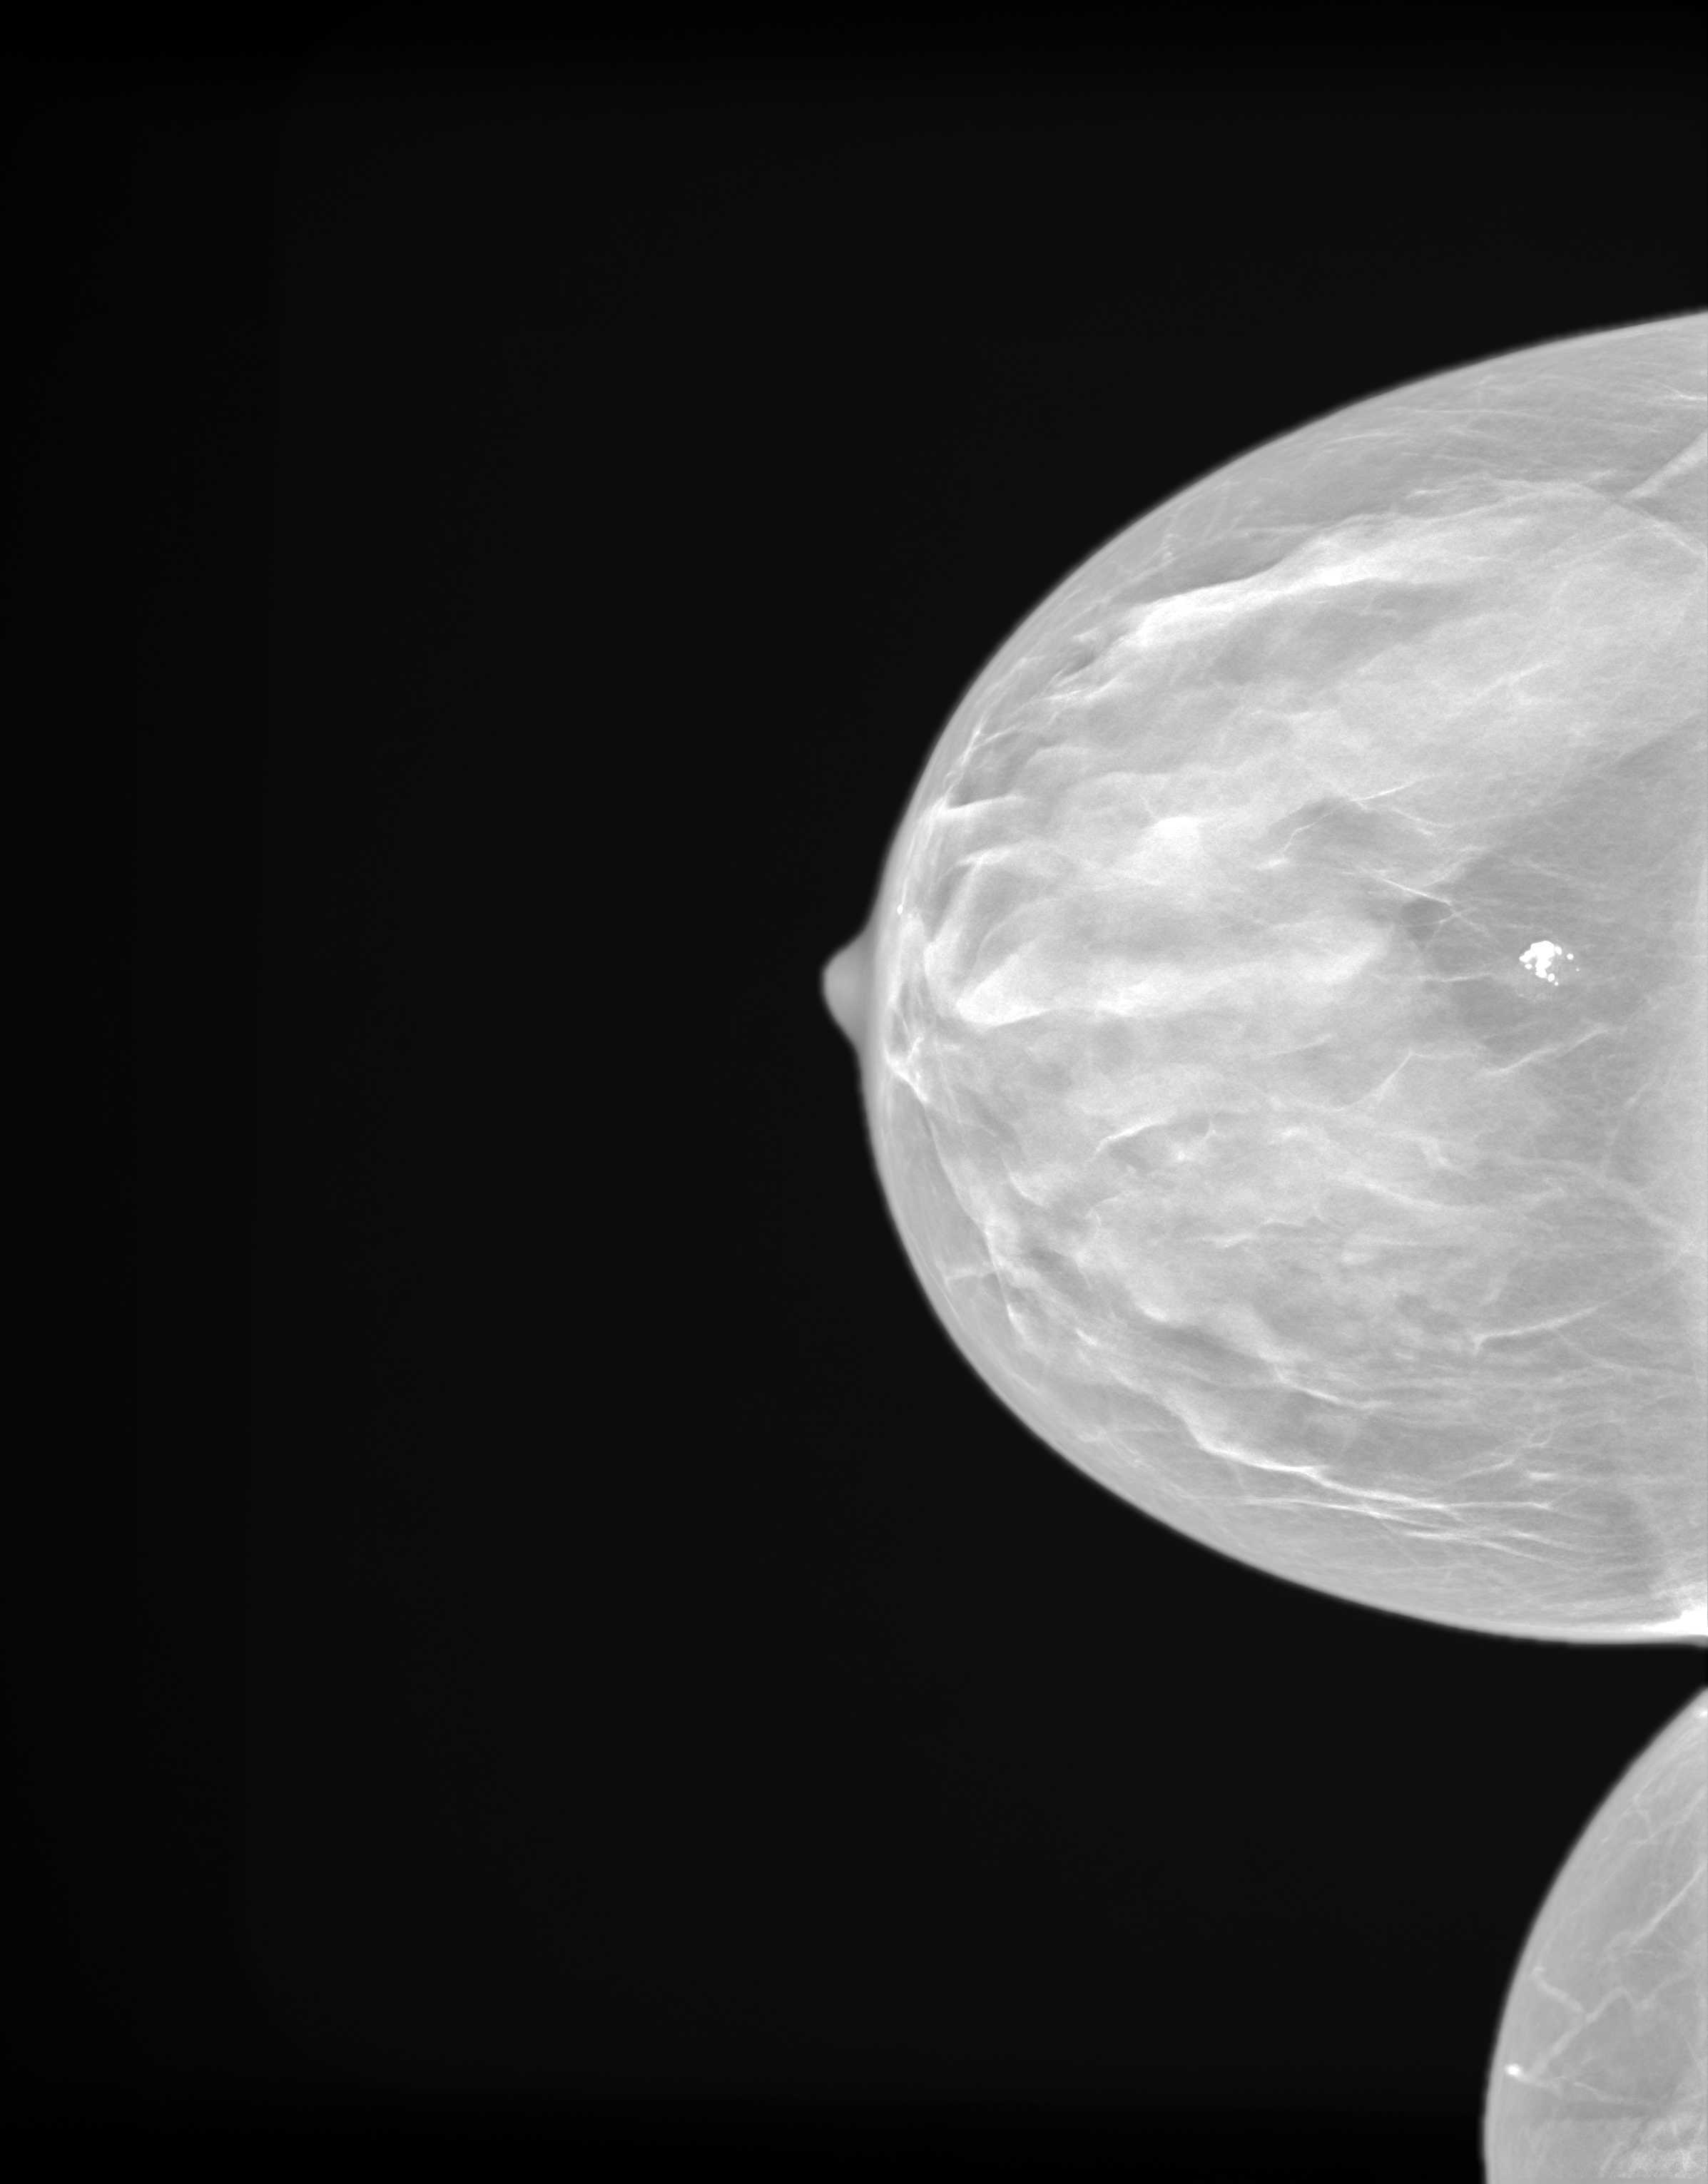
Screening examination. Patient: female, 61 years.
Image type: synthesized 2-D view from tomosynthesis. Breast: right. Projection: craniocaudal (CC) view.